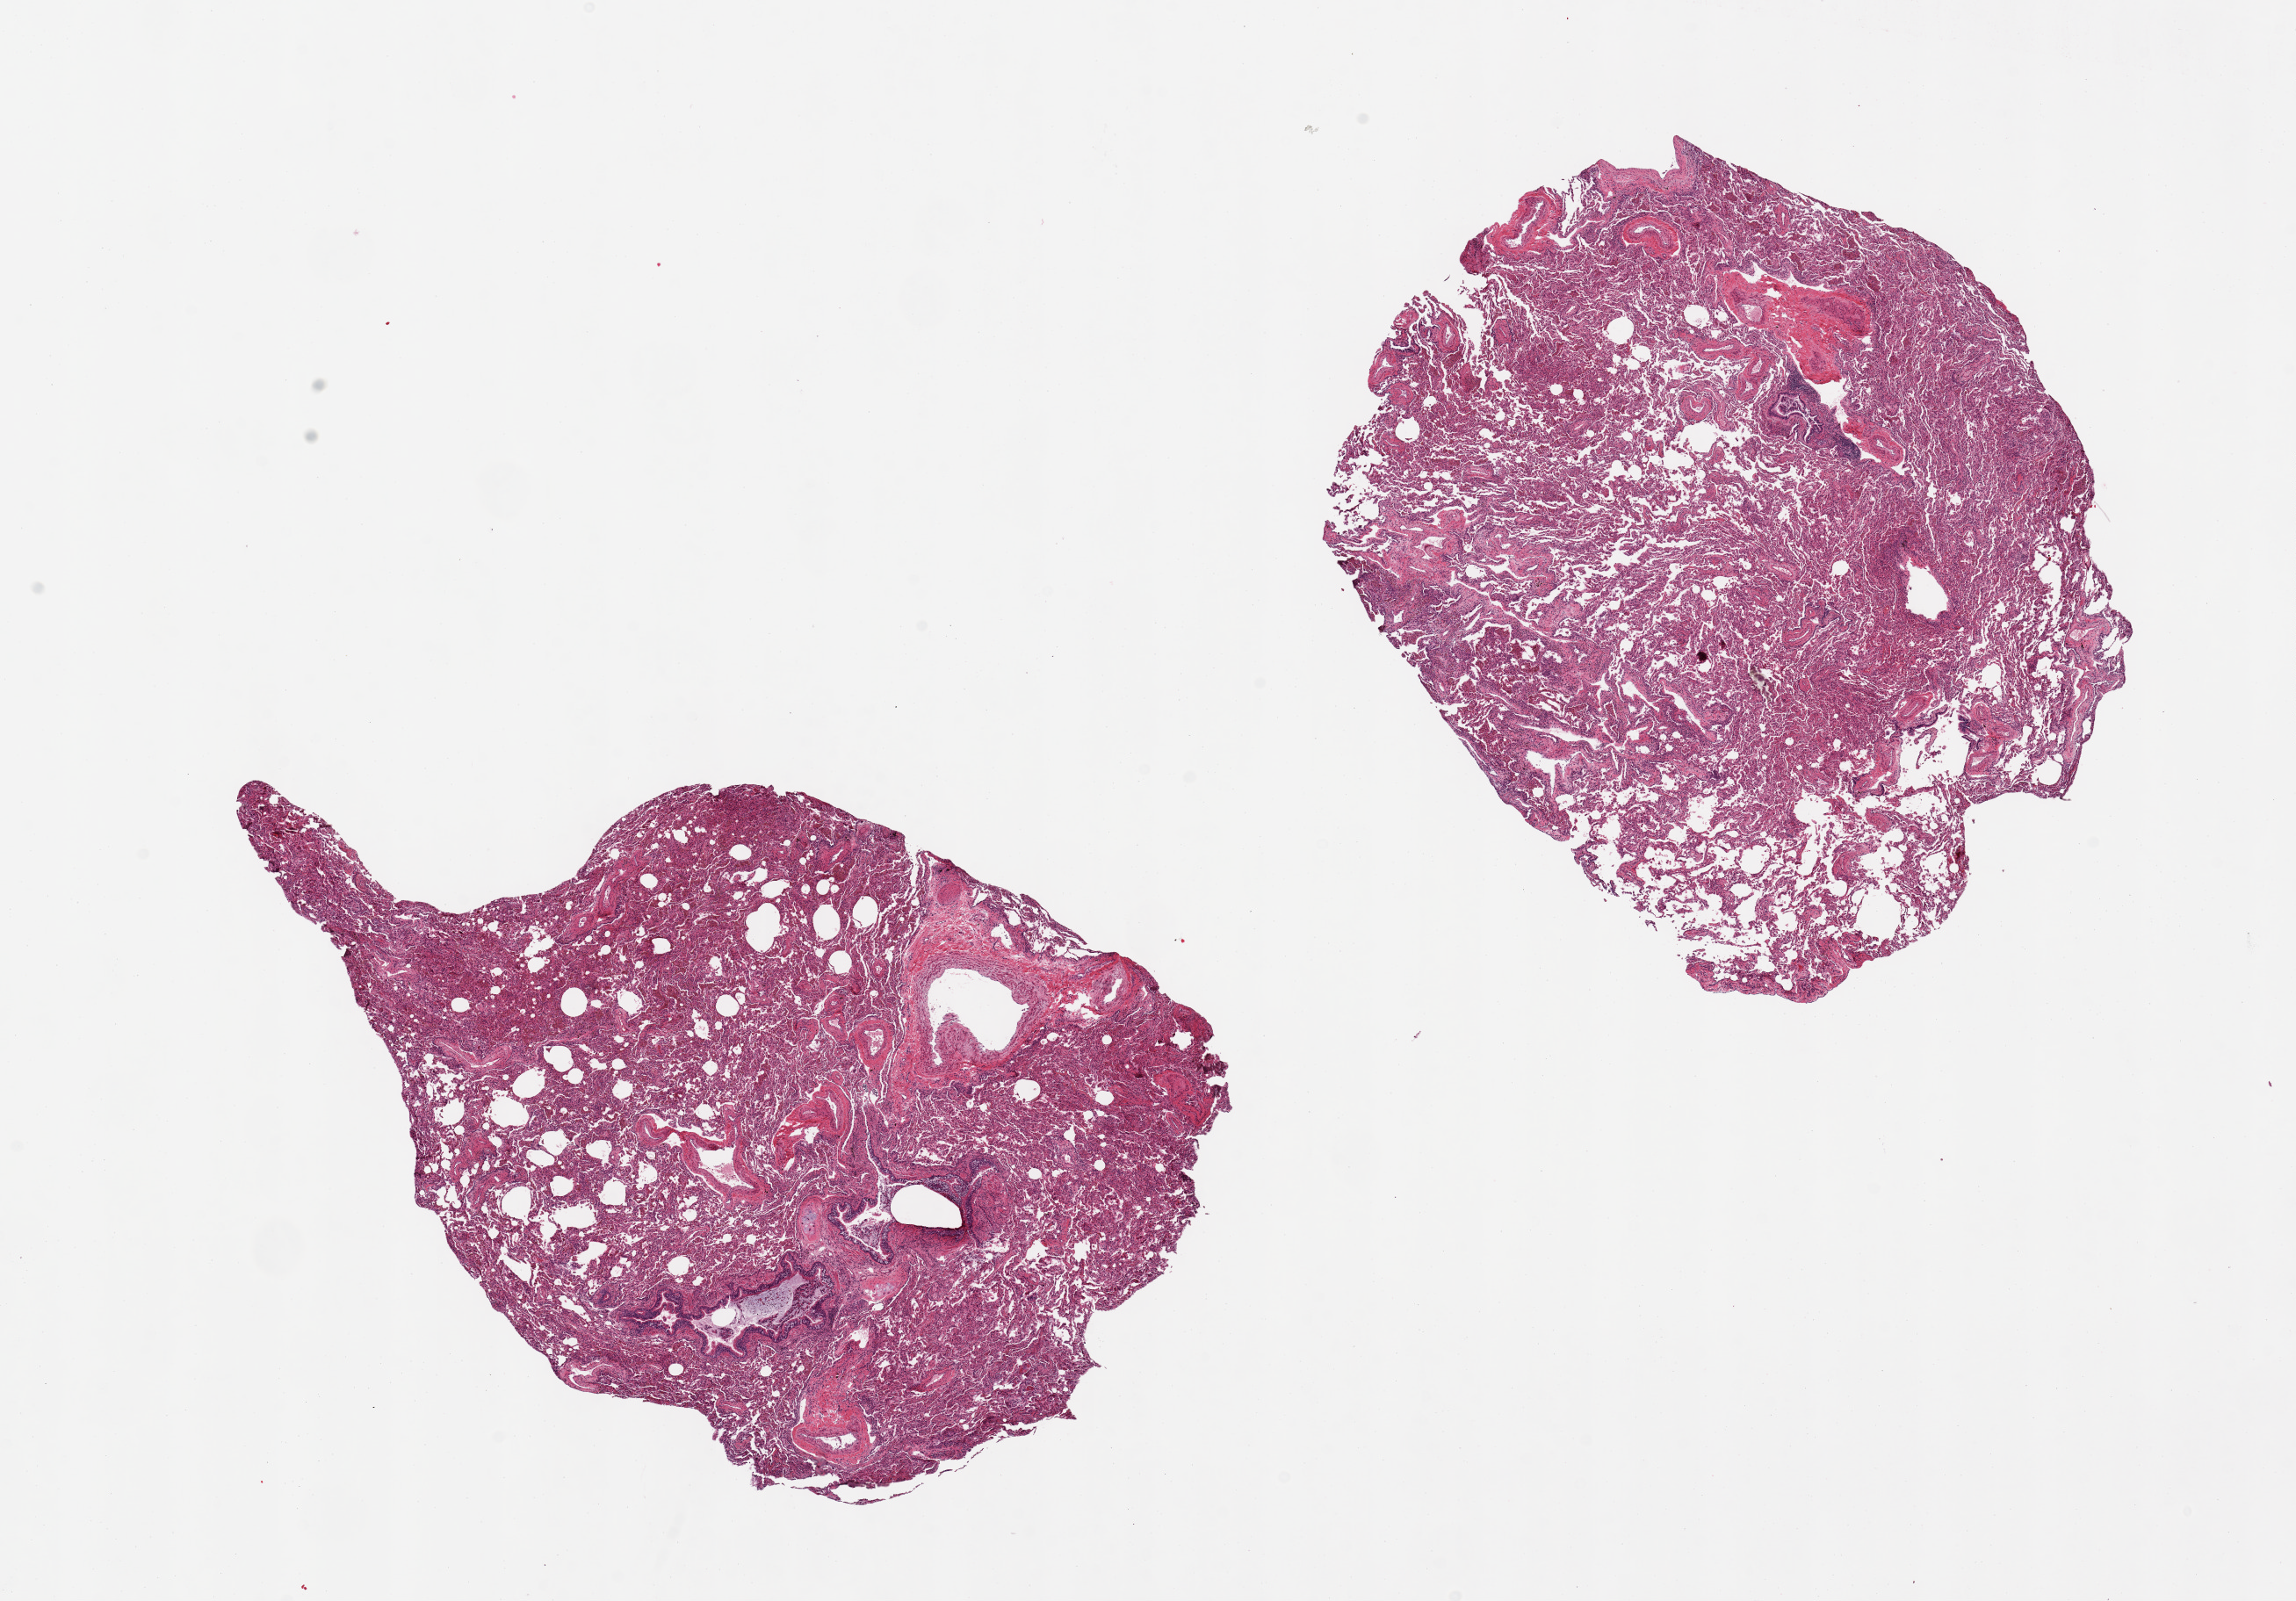
Haematoxylin and eosin whole-slide image — whole scanned area (about 20.7 x 14.4 mm, slide scanned at 20x) shown as a low-resolution overview, PAXgene-fixed, paraffin-embedded tissue, sampled site (target tissue): lung, donor tissue sample. Female donor.
Reviewer comment on this tissue sample: 2 pieces, 9x6 & 7x6.5mm; patchy chronic and active pneumonitis.